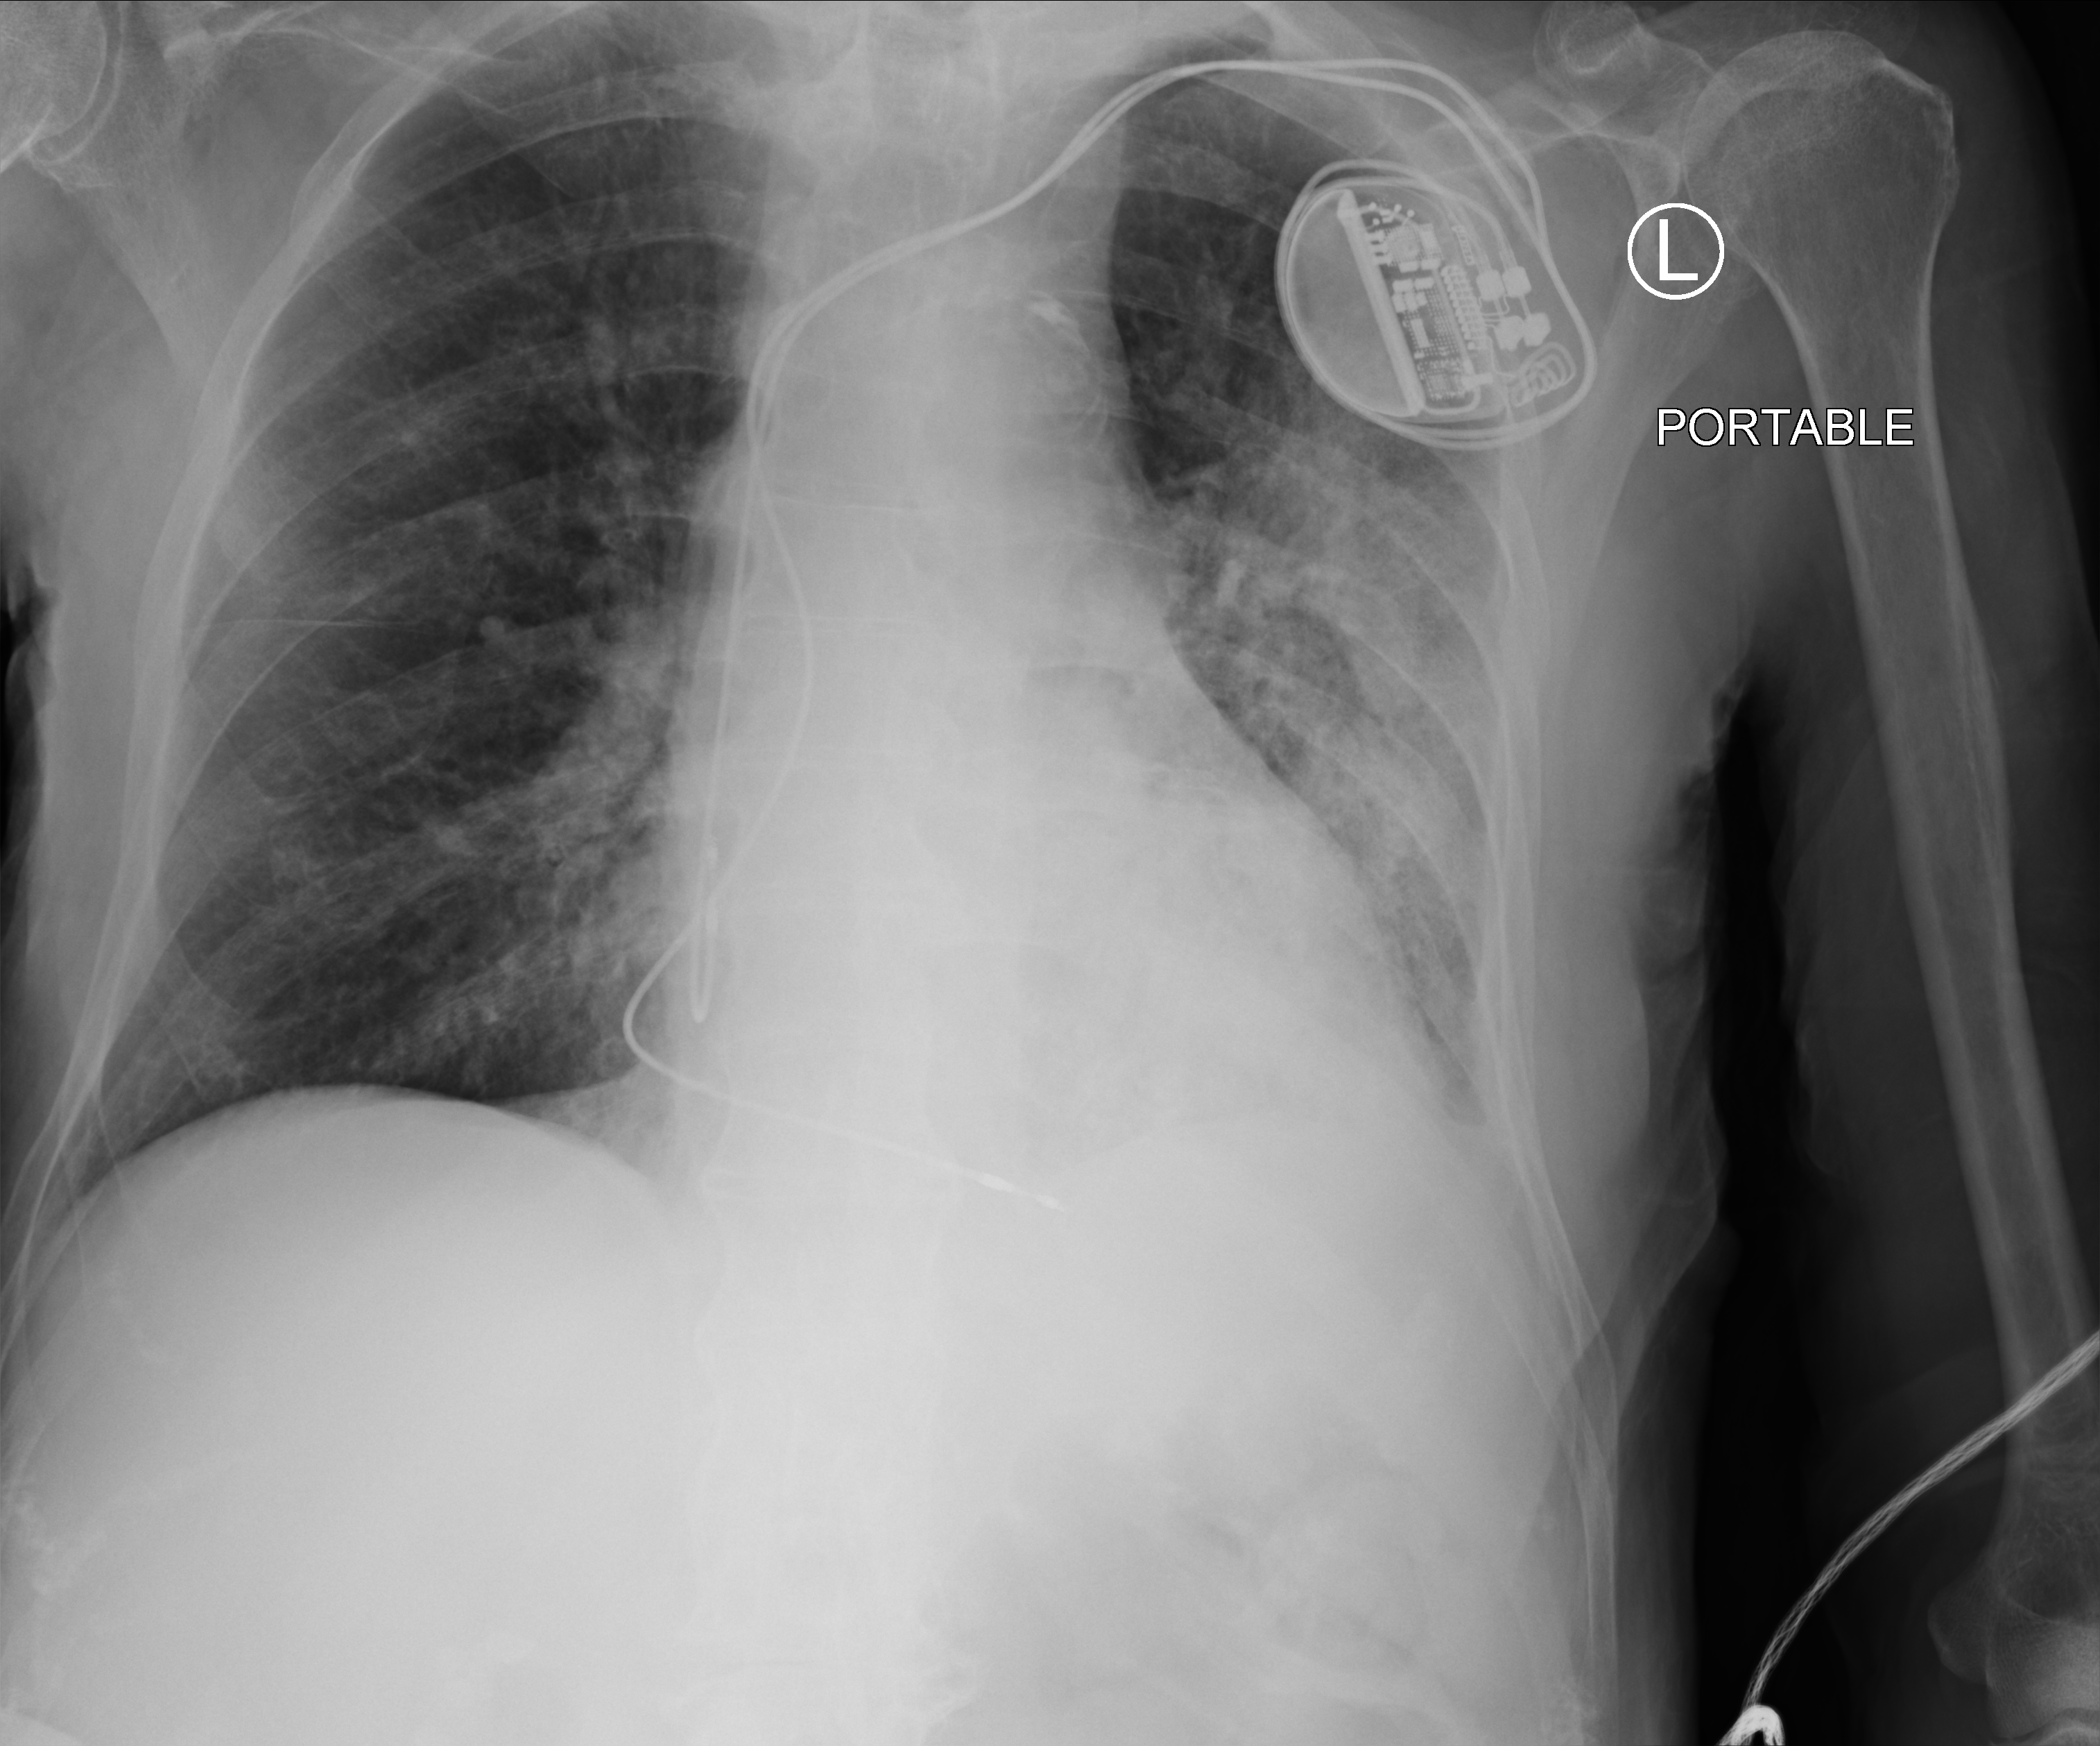
Chest X-ray (portable). Male patient hospitalised with COVID-19, age 75–90 years.
Admission-level facts for this patient (not findings on this image; timing relative to this image not recorded):
- length of hospital stay: 5 days
- other chronic lung disease (admission record): no